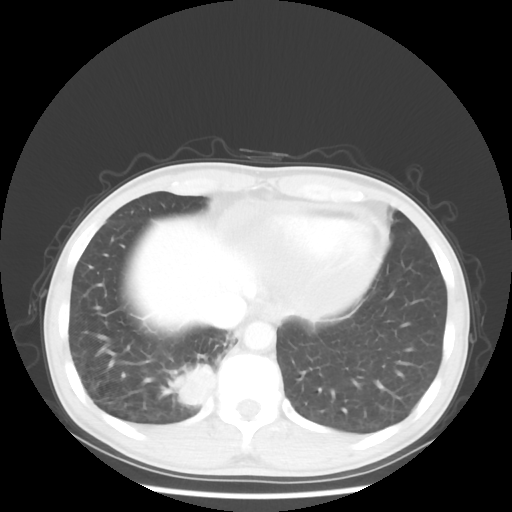
Chest CT, one axial slice. Position 10 of 58 along the scan axis. Lung window (W 1500 / L -600 HU). 512 × 512 image matrix, field of view 360 × 360 mm. Patient: male, 56 years. Case-level facts recorded for this patient, not image findings: clinical TNM (as recorded): T2 N1 M1.
Outlined on this slice (rectangle marked by the reading radiologist):
- lung tumour (recorded histology: adenocarcinoma): bounding box (x1, y1, x2, y2) in pixels: (171, 358, 218, 415)